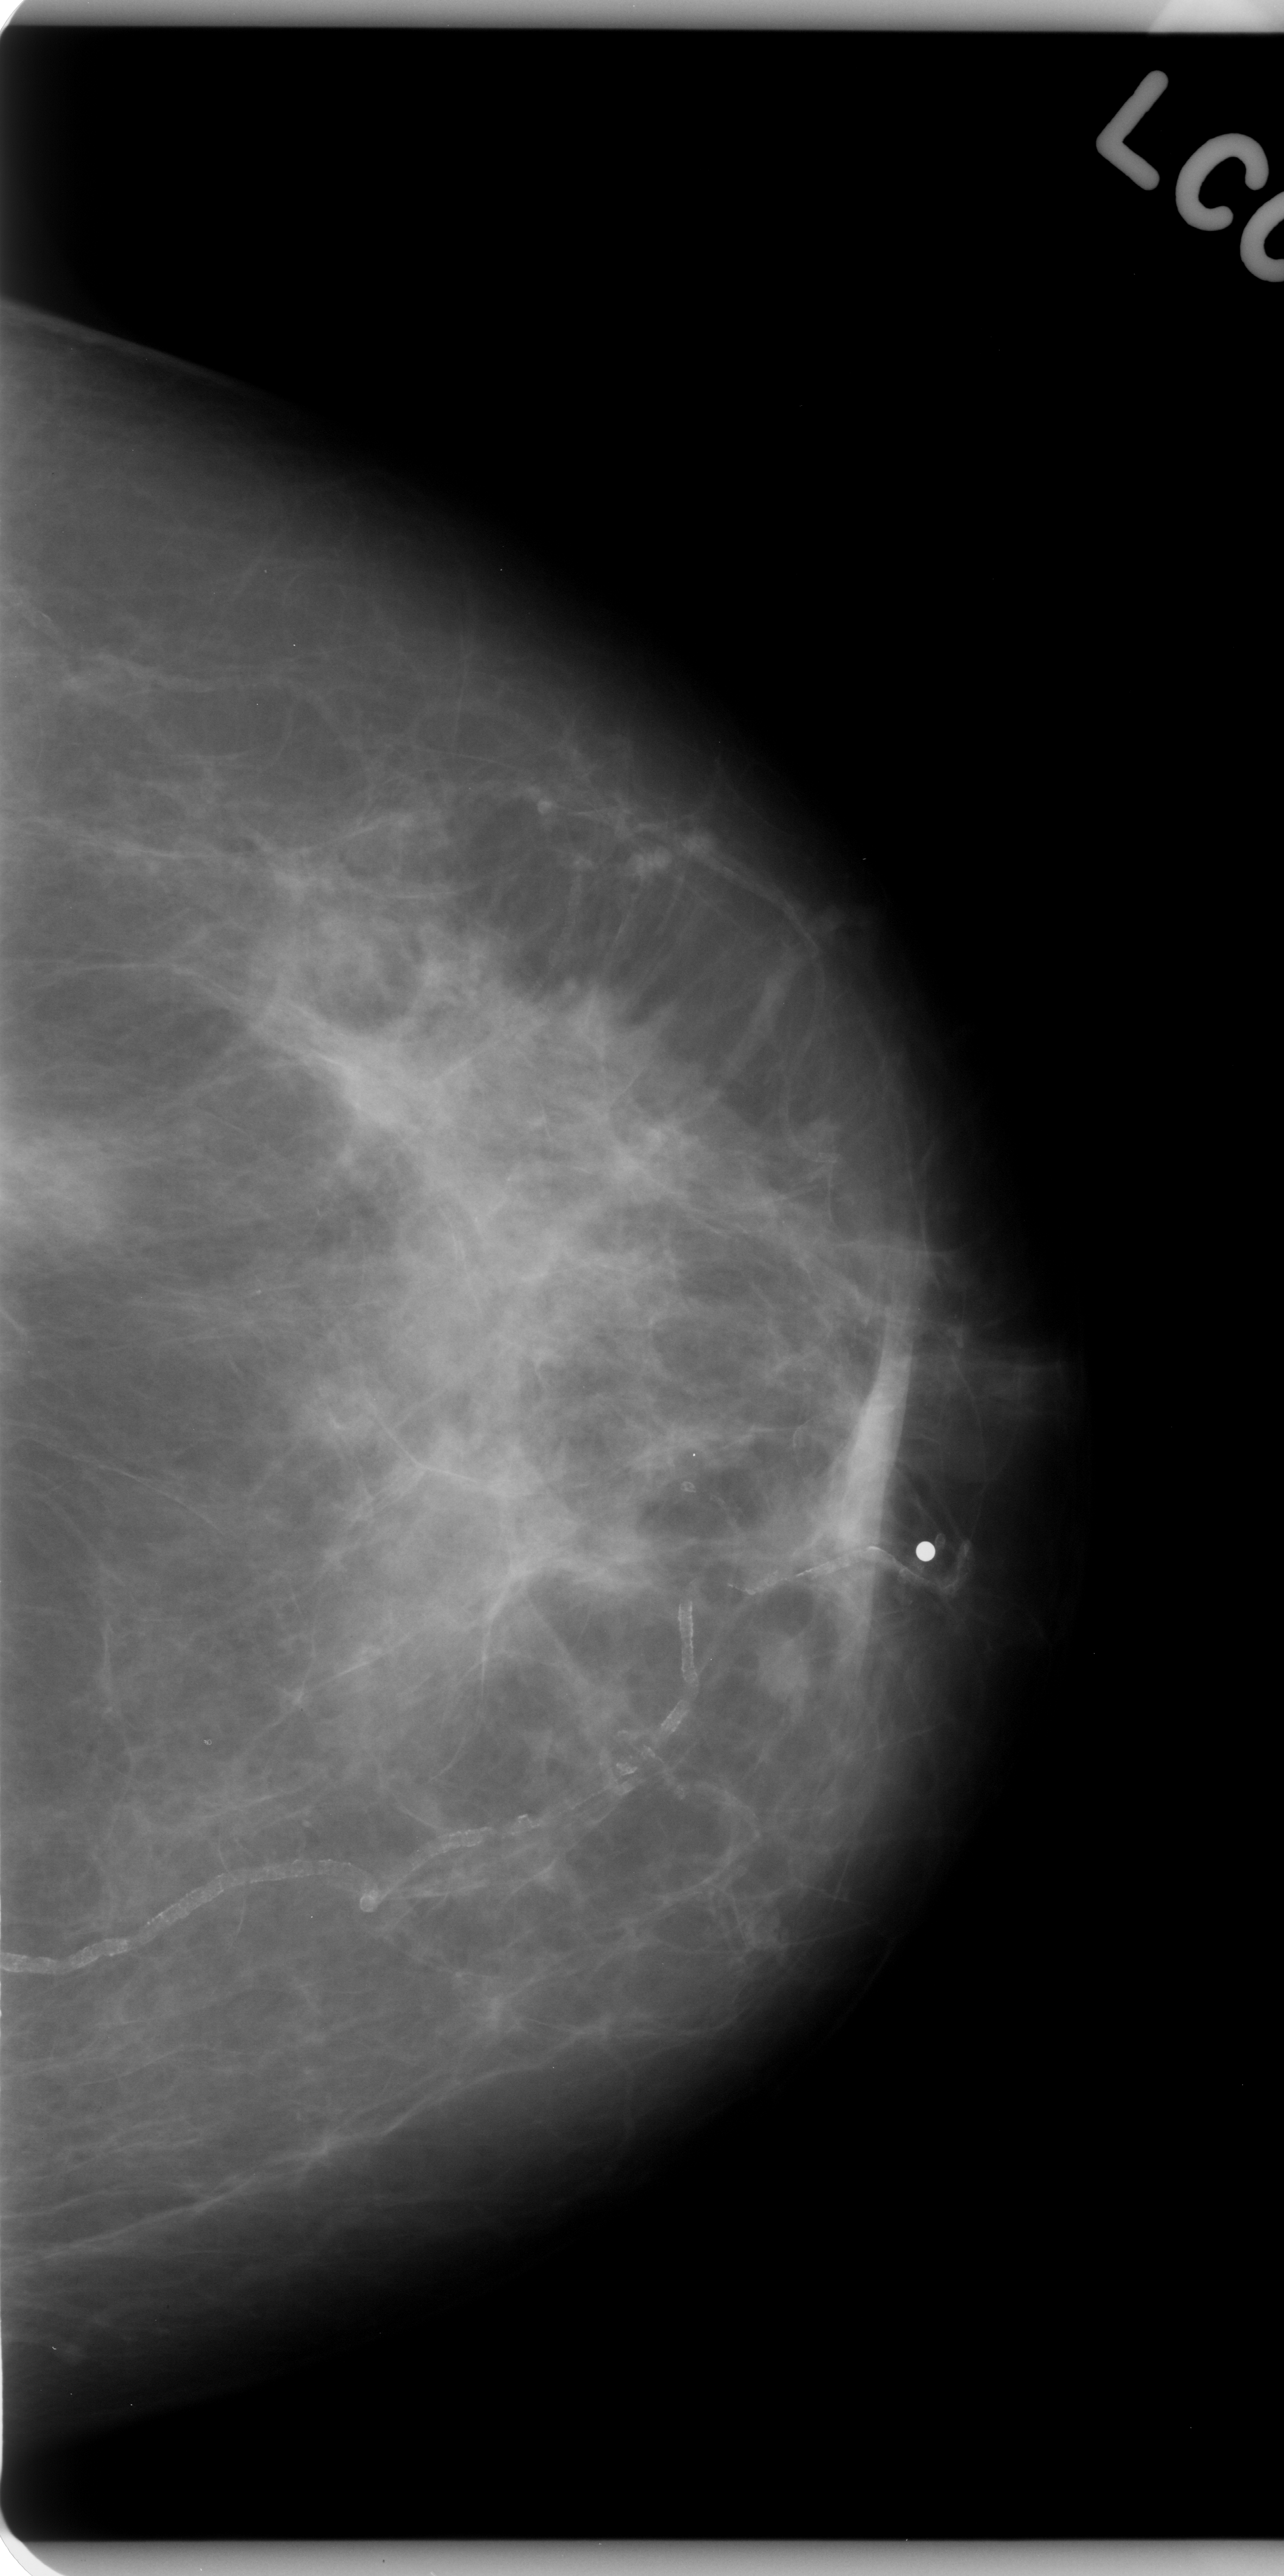
Digitized screen-film mammogram. Left breast. CC view. Breast composition: scattered fibroglandular densities (BI-RADS density category 2 of 4). 1284 × 2576 image matrix.
Expert-marked regions of interest on this film, with their recorded descriptors:
- Finding 1 of 2: mass, shape oval, margins ill defined; BI-RADS assessment category 4; subtlety rating 4 on a 1 (subtle) to 5 (obvious) scale; pathology (as recorded): malignant: bounding box (x1, y1, x2, y2) in pixels: (0, 1103, 155, 1279)
- Finding 2 of 2: mass, shape irregular, margins ill defined; BI-RADS assessment category 5; subtlety rating 4 on a 1 (subtle) to 5 (obvious) scale; pathology result (as recorded, not read from the image): malignant: (727, 1440, 946, 1657)